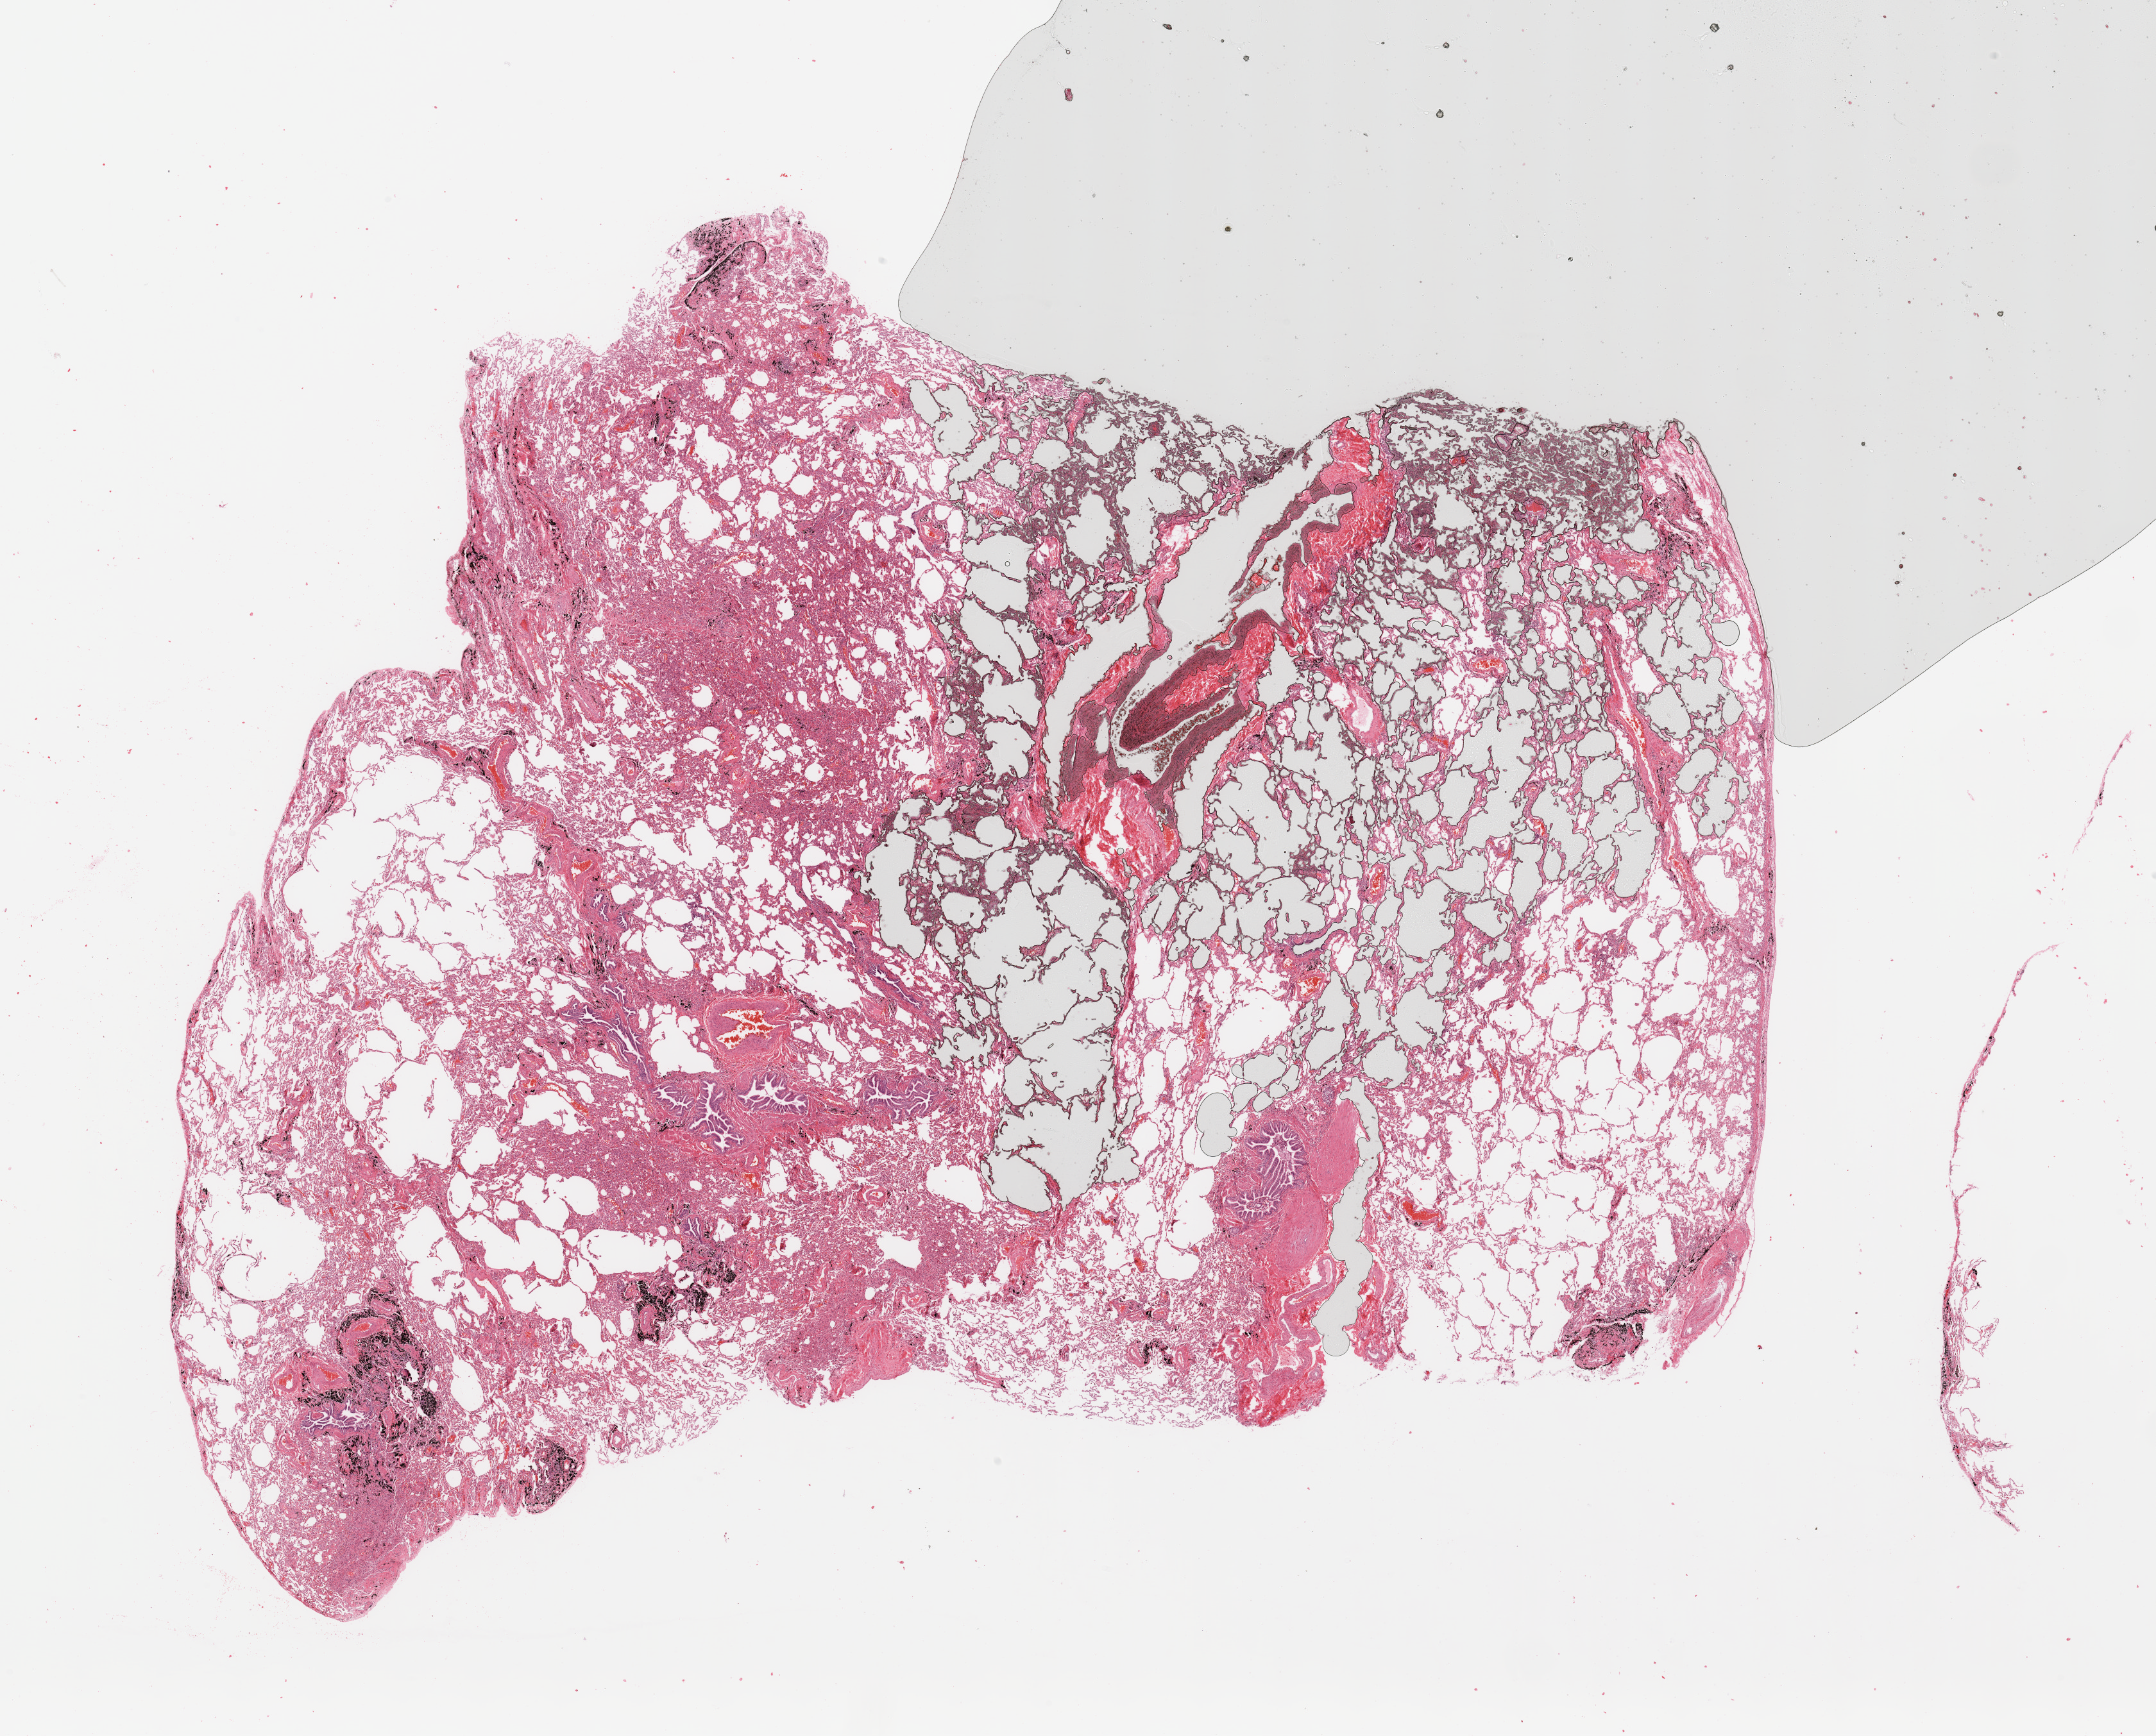
Digitized H&E tissue section (whole slide) — whole scanned area (about 26.6 x 21.4 mm, slide scanned at 20x) shown as a low-resolution overview, normal (non-tumour) tissue sample, sampled site: lung. 58-year-old male patient.
This section: normal (non-tumour) tissue from the same patient. Patient diagnosis: Adenocarcinoma, NOS.